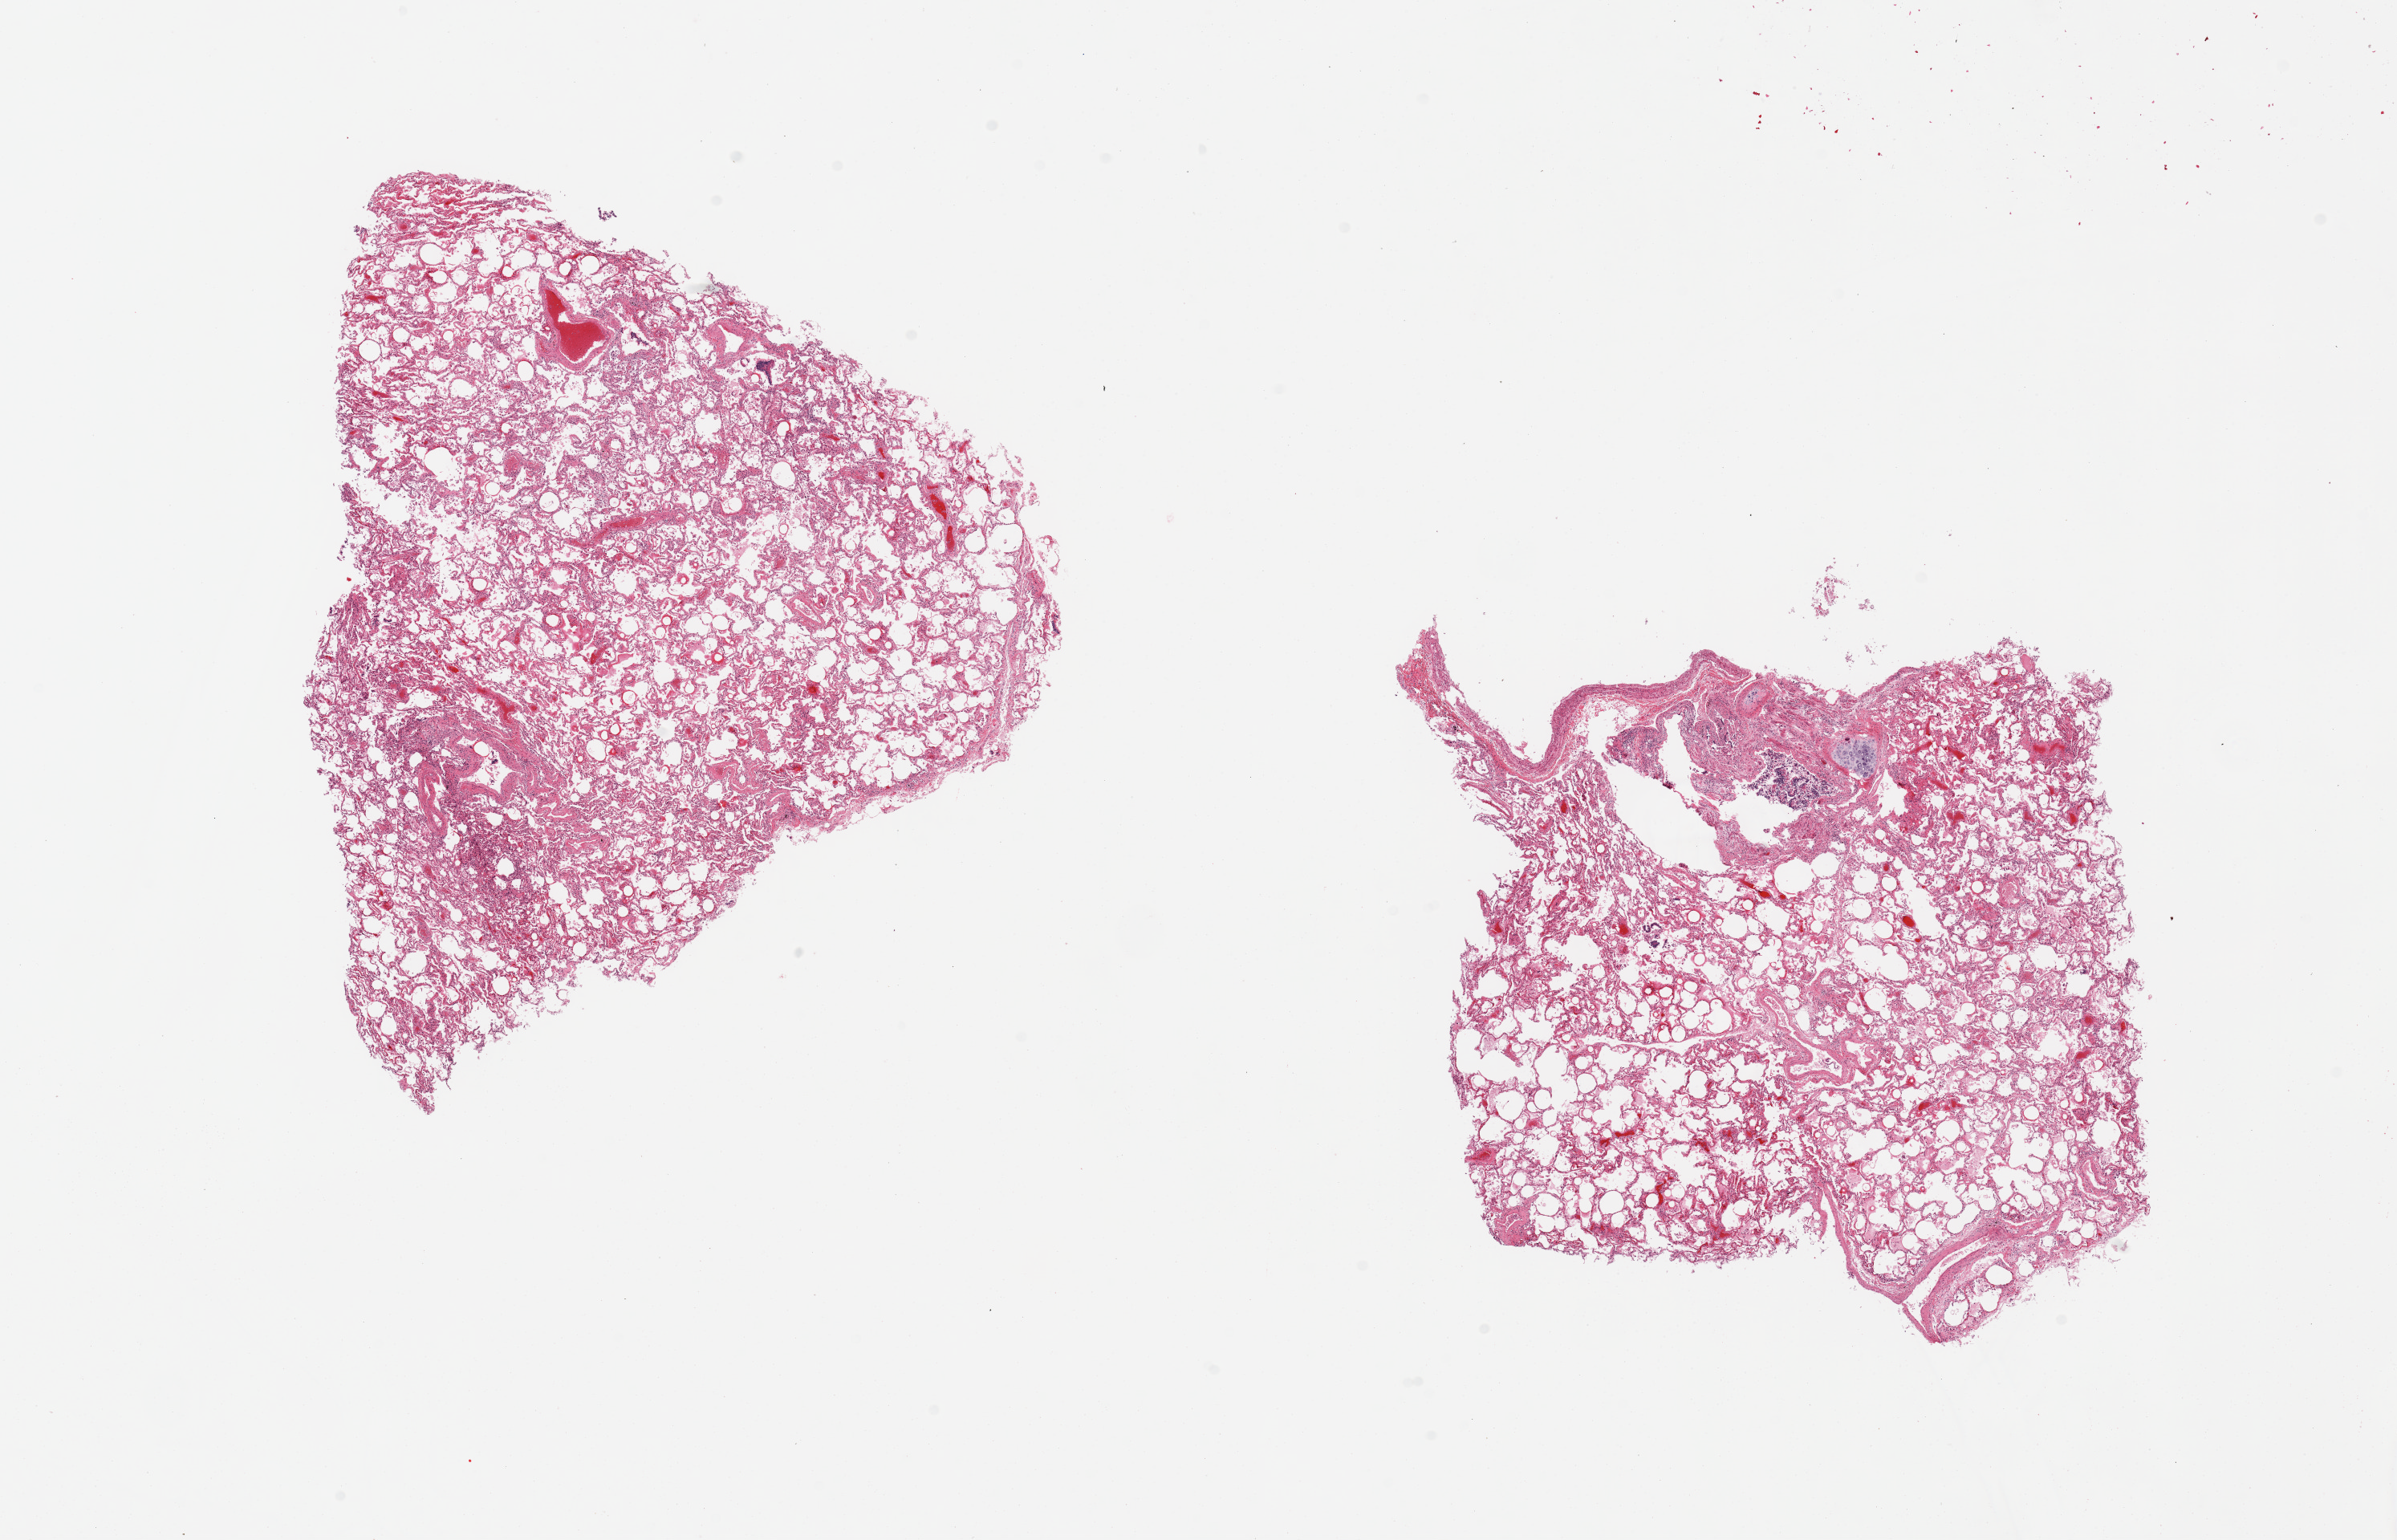
Whole-slide image, hematoxylin and eosin (H&E) stain — shown as a low-resolution overview of the whole scanned area (about 23.6 x 15.2 mm); PAXgene-fixed, paraffin-embedded tissue; sampled site (target tissue): lung; tissue donor sample.
Review note (as recorded): 2 pieces; congestion, focally attached fragment of vessel wall, cartilage and sloughed bronchial epithelium.